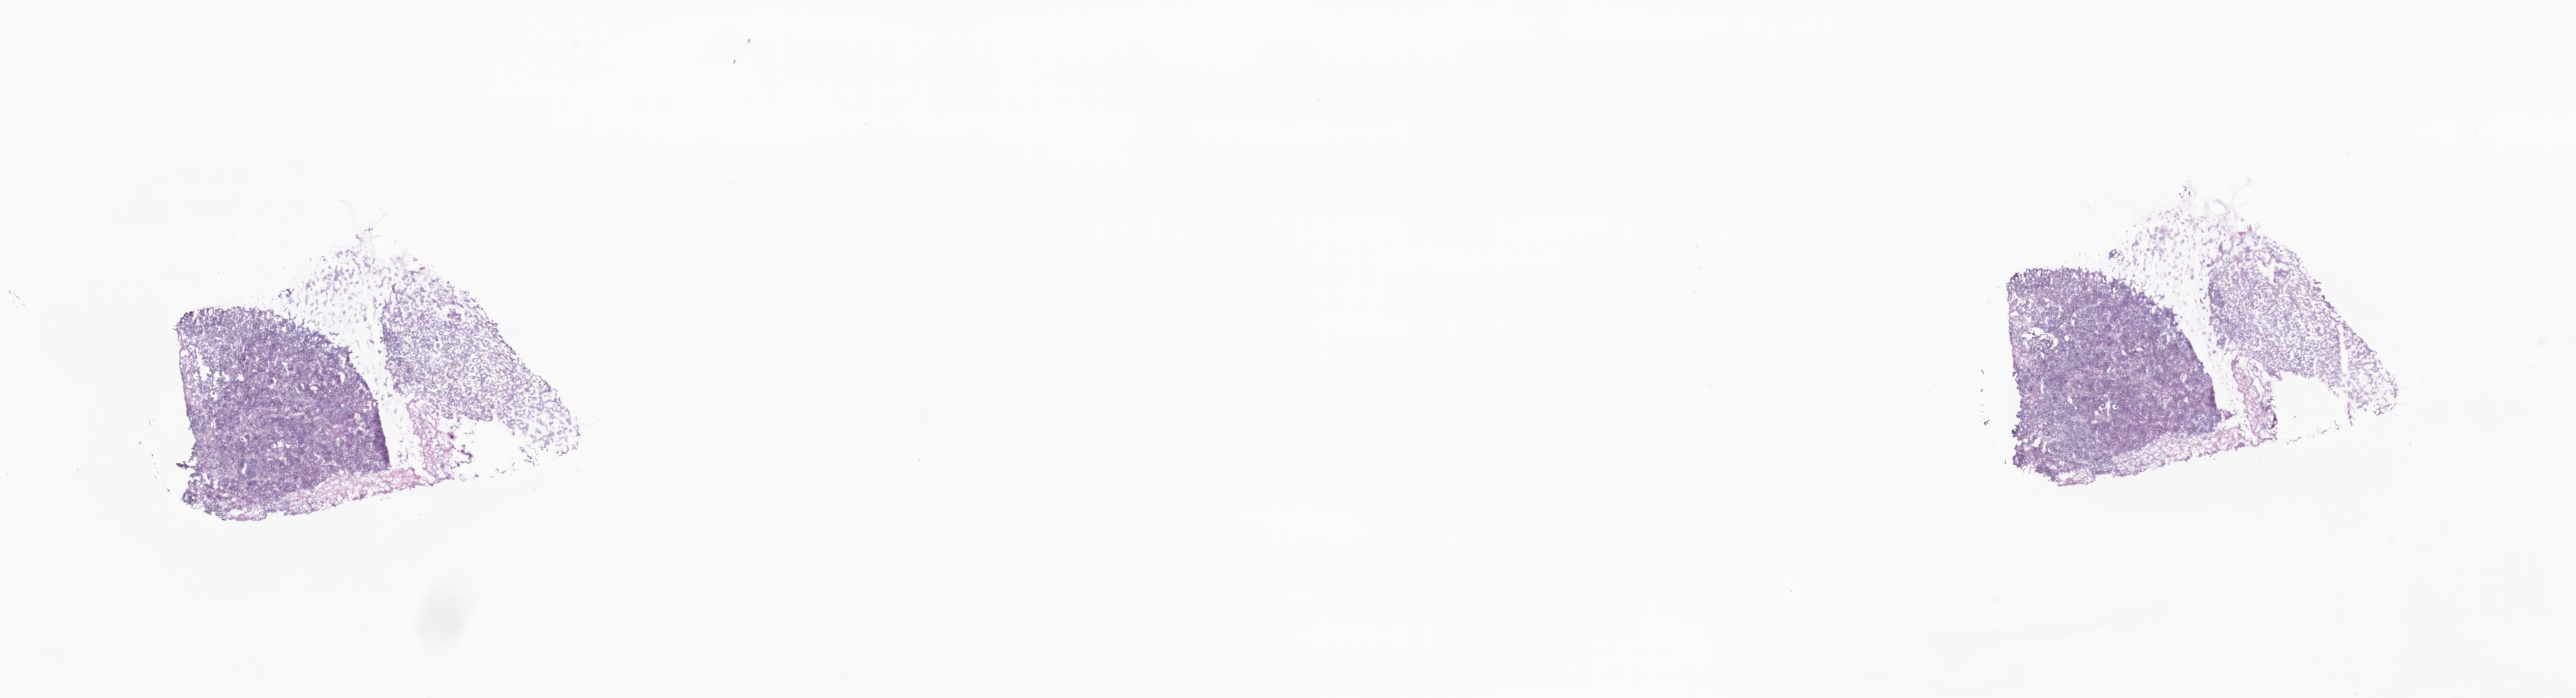
Hematoxylin and eosin (H&E) whole-slide image, low-resolution overview of the scanned area, about 27.2 x 7.4 mm. Cryosection. Metastatic tumor tissue, resected from lymph nodes of inguinal region or leg. Male patient; age at initial diagnosis 45 years.
Patient diagnosis (primary): Malignant melanoma, NOS.